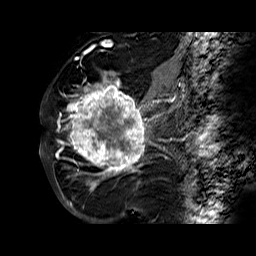
Breast MRI (dynamic contrast-enhanced), one sagittal slice; slice 37 of 60 in the series (ordered by position); dynamic contrast-enhanced series, time point 2 of 6 at this slice position (early post-contrast); 1.5 T; TE 6.3 ms, TR 32.4 ms; 4 mm slice thickness; 256 × 256 image matrix, field of view 200 × 200 mm. Female patient. From the clinical record (not read from this slice): setting: breast cancer imaged before/during neoadjuvant chemotherapy; receptor status: HR-positive, HER2-negative.
Outlined on this slice (semi-automatically segmented with operator editing):
- analysis volume of interest (the breast-tissue region the enhancement analysis was run in; not a lesion): box from (x=68, y=72) to (x=177, y=183) px
- tumour enhancement mask (voxels above the 100 % enhancement threshold inside the analysis volume of interest): (x=68, y=72)–(x=170, y=183)